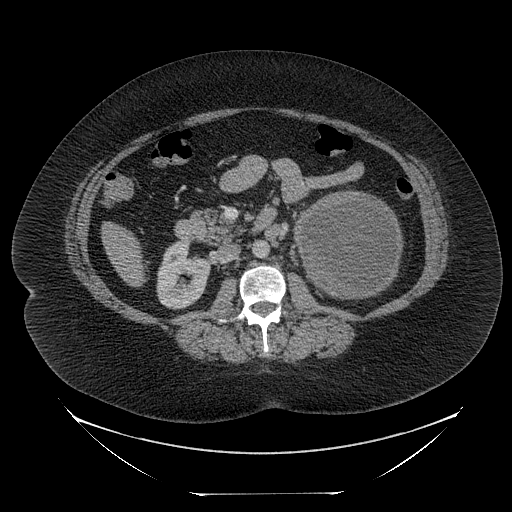
Contrast-enhanced abdominal CT, one axial slice. Slice 121 of 205 in the series (ordered by position). Reconstruction kernel STANDARD. 120 kVp. Soft-tissue window (W 400 / L 40 HU). 2.5 mm slice thickness. 512 × 512 image matrix, field of view 500 × 500 mm. Patient: female, 53 years. From the clinical record (not read from this slice): diagnosis: adrenocortical carcinoma; tumour side: left adrenal; tumour size at pathology: 17 cm; Ki-67 index: 20 %; stage (as recorded): 3.
Annotated regions visible in this slice (semi-automatically segmented with operator editing):
- mass: bounding box (x1, y1, x2, y2) in pixels: (301, 194, 401, 296)